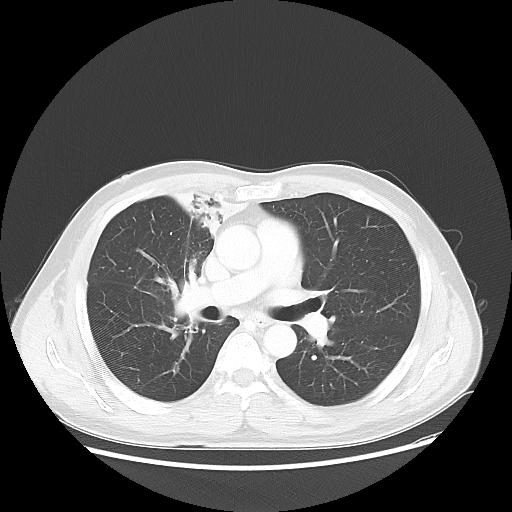
Chest CT, one axial slice. Slice 31 of 56 in the series (ordered by position). Reconstruction kernel LUNG. 100 kVp. Lung window (W 1500 / L -600 HU). 5 mm slice thickness. 512 × 512 image matrix, field of view 398 × 398 mm. Patient: male, 60 years. From the clinical record (not read from this slice): clinical TNM (as recorded): T2a N1 M0.
Outlined on this slice (bounding box drawn by a radiologist):
- lung tumour (recorded histology: squamous cell carcinoma): box from (x=160, y=177) to (x=254, y=244) px